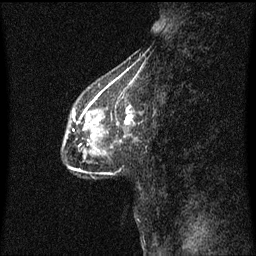
Breast MRI (dynamic contrast-enhanced), one sagittal slice. Position 19 of 60 along the scan axis. Dynamic contrast-enhanced series, image 2 of 3 at this slice position (ordered by acquisition). 1.5 T. TE 4.2 ms, TR 8.4 ms. 2 mm slice thickness. 256 × 256 image matrix. Patient: female, 49 years. From the clinical record (not read from this slice): setting: breast cancer imaged before/during neoadjuvant chemotherapy; receptor status: HR-positive, HER2-negative.
Outlined on this slice (semi-automatically segmented with operator editing):
- analysis volume of interest (the breast-tissue region the enhancement analysis was run in; not a lesion): bounding box [x1, y1, x2, y2] px = [64, 108, 140, 158]
- tumour enhancement mask (voxels above the 70 % enhancement threshold inside the analysis volume of interest): [93, 118, 129, 137]